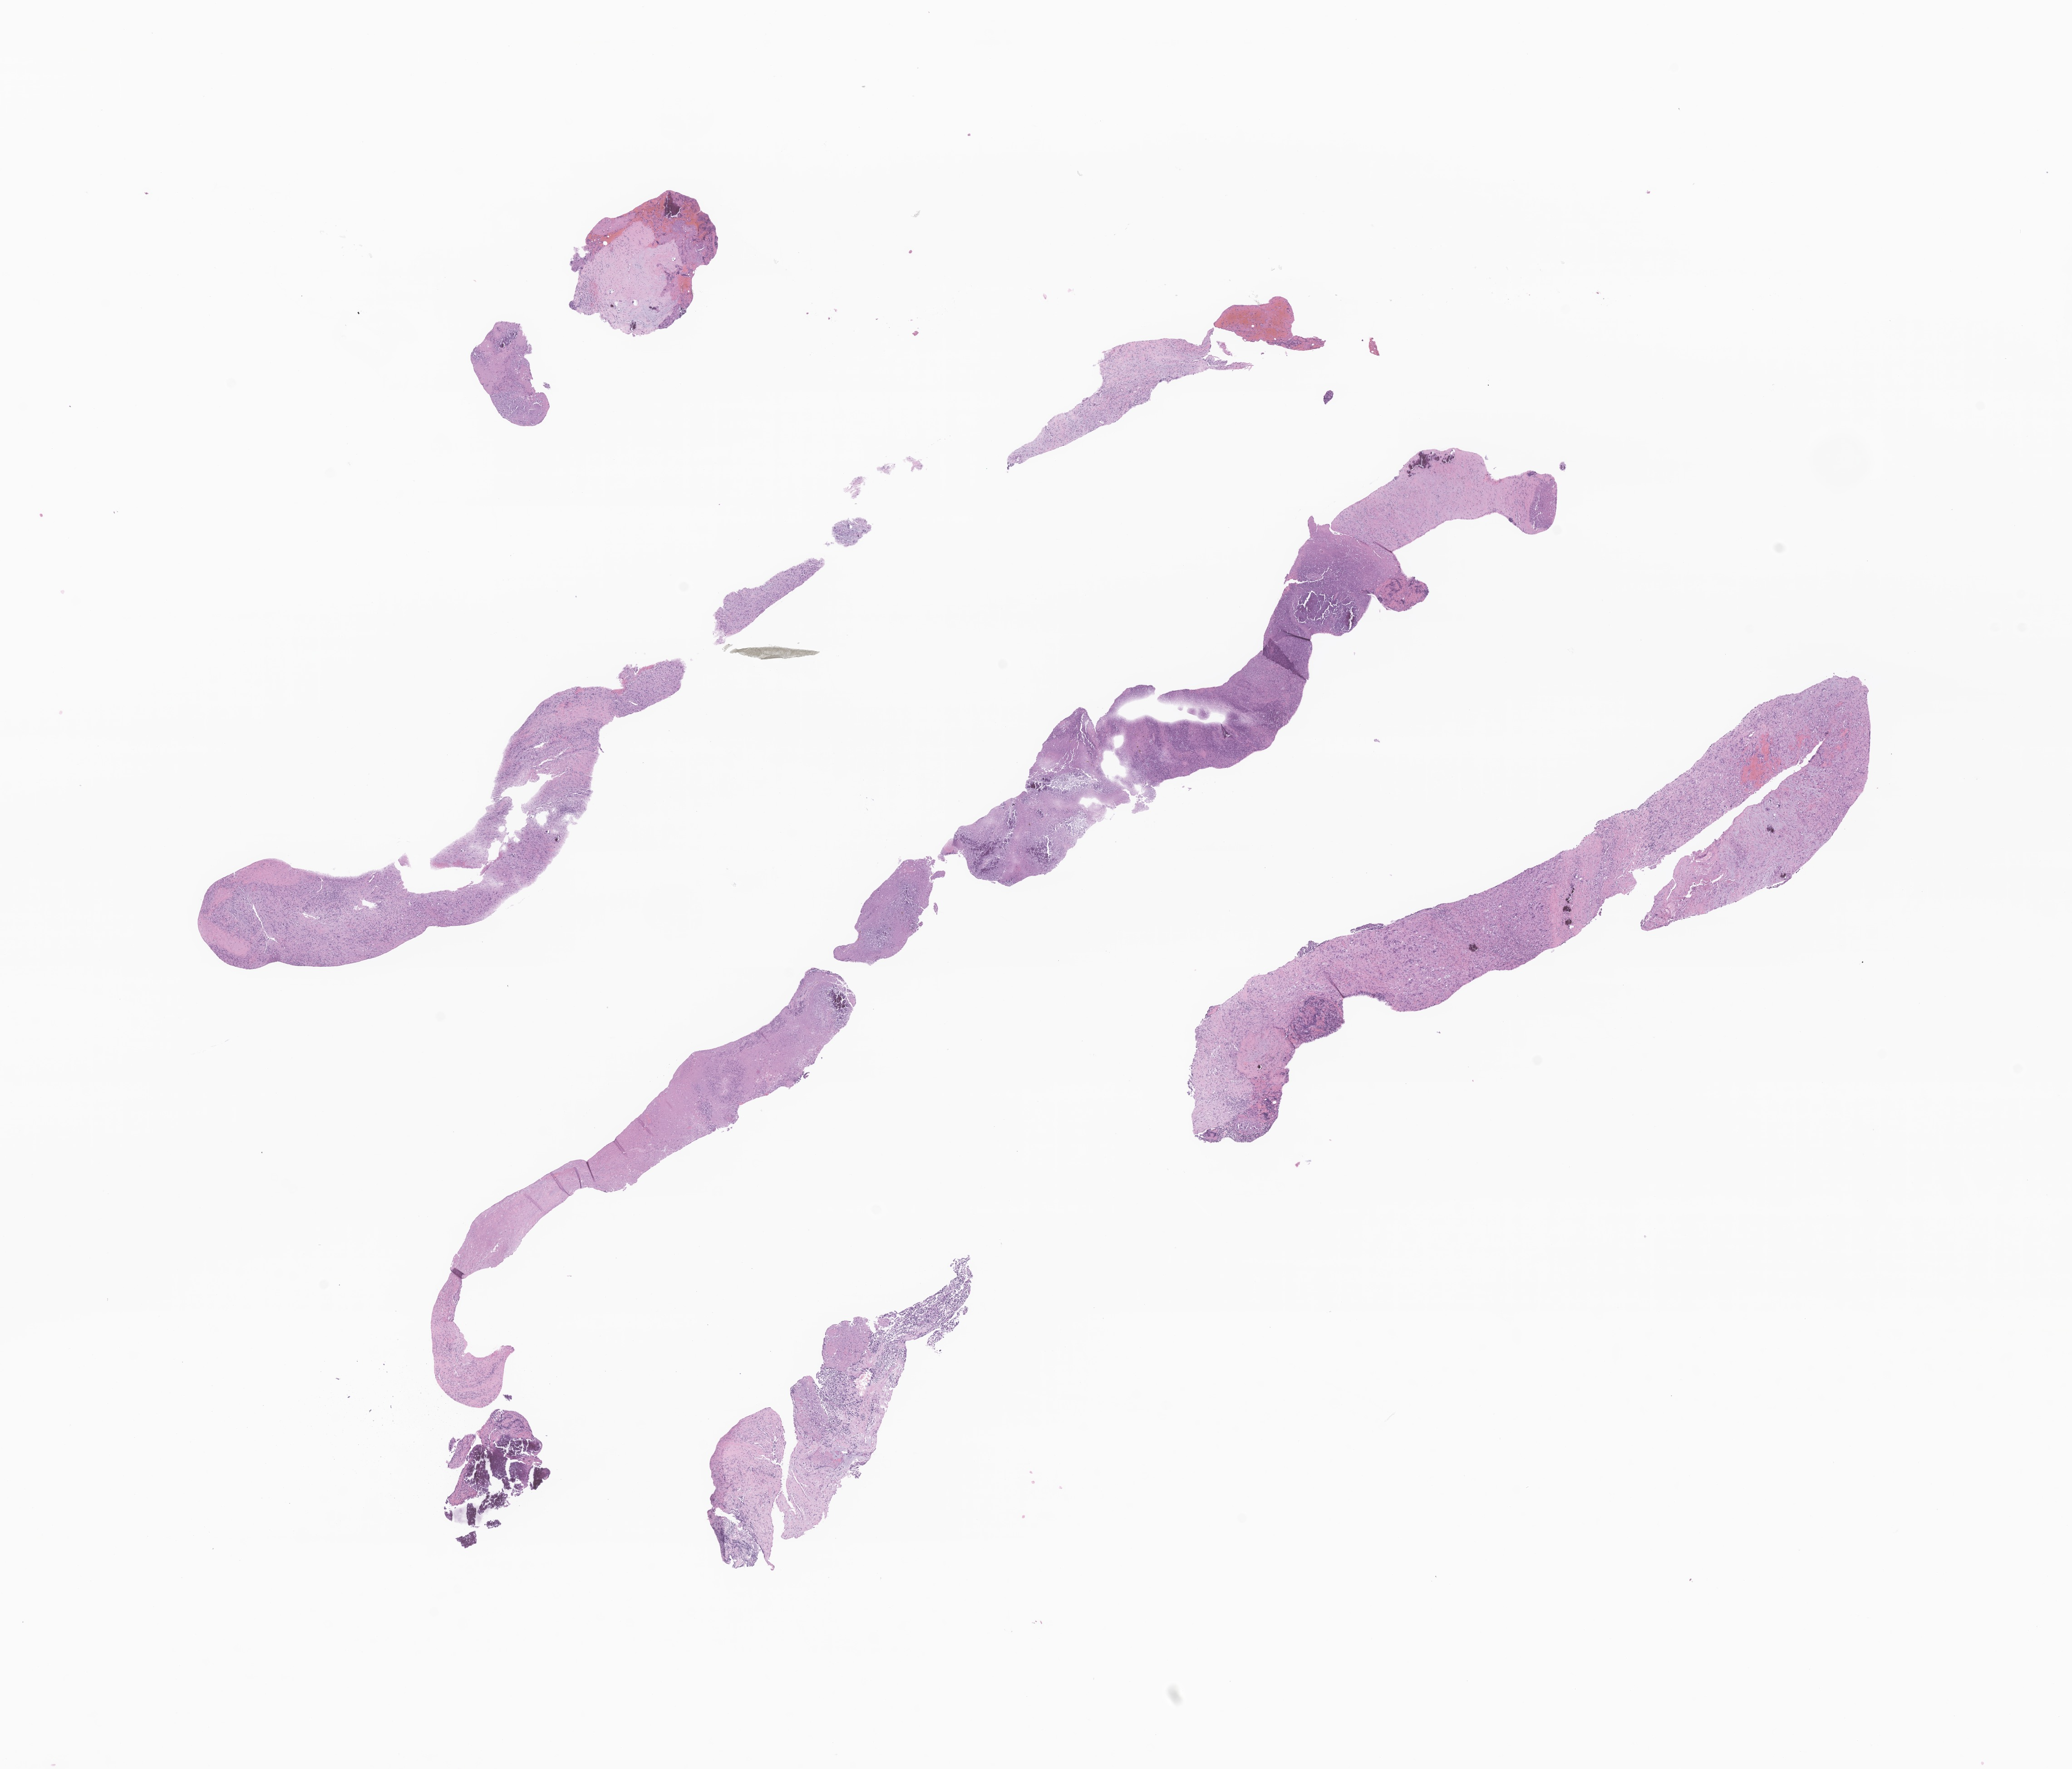
Digitized hematoxylin and eosin (H&E)-stained section of tumor tissue from the adrenal gland — low-resolution overview of the scanned area, about 19.2 x 16.4 mm. Formalin-fixed paraffin-embedded section. Patient male; age 36 months.
- diagnosis (ICD-O-3 morphology term): Ganglioneuroblastoma